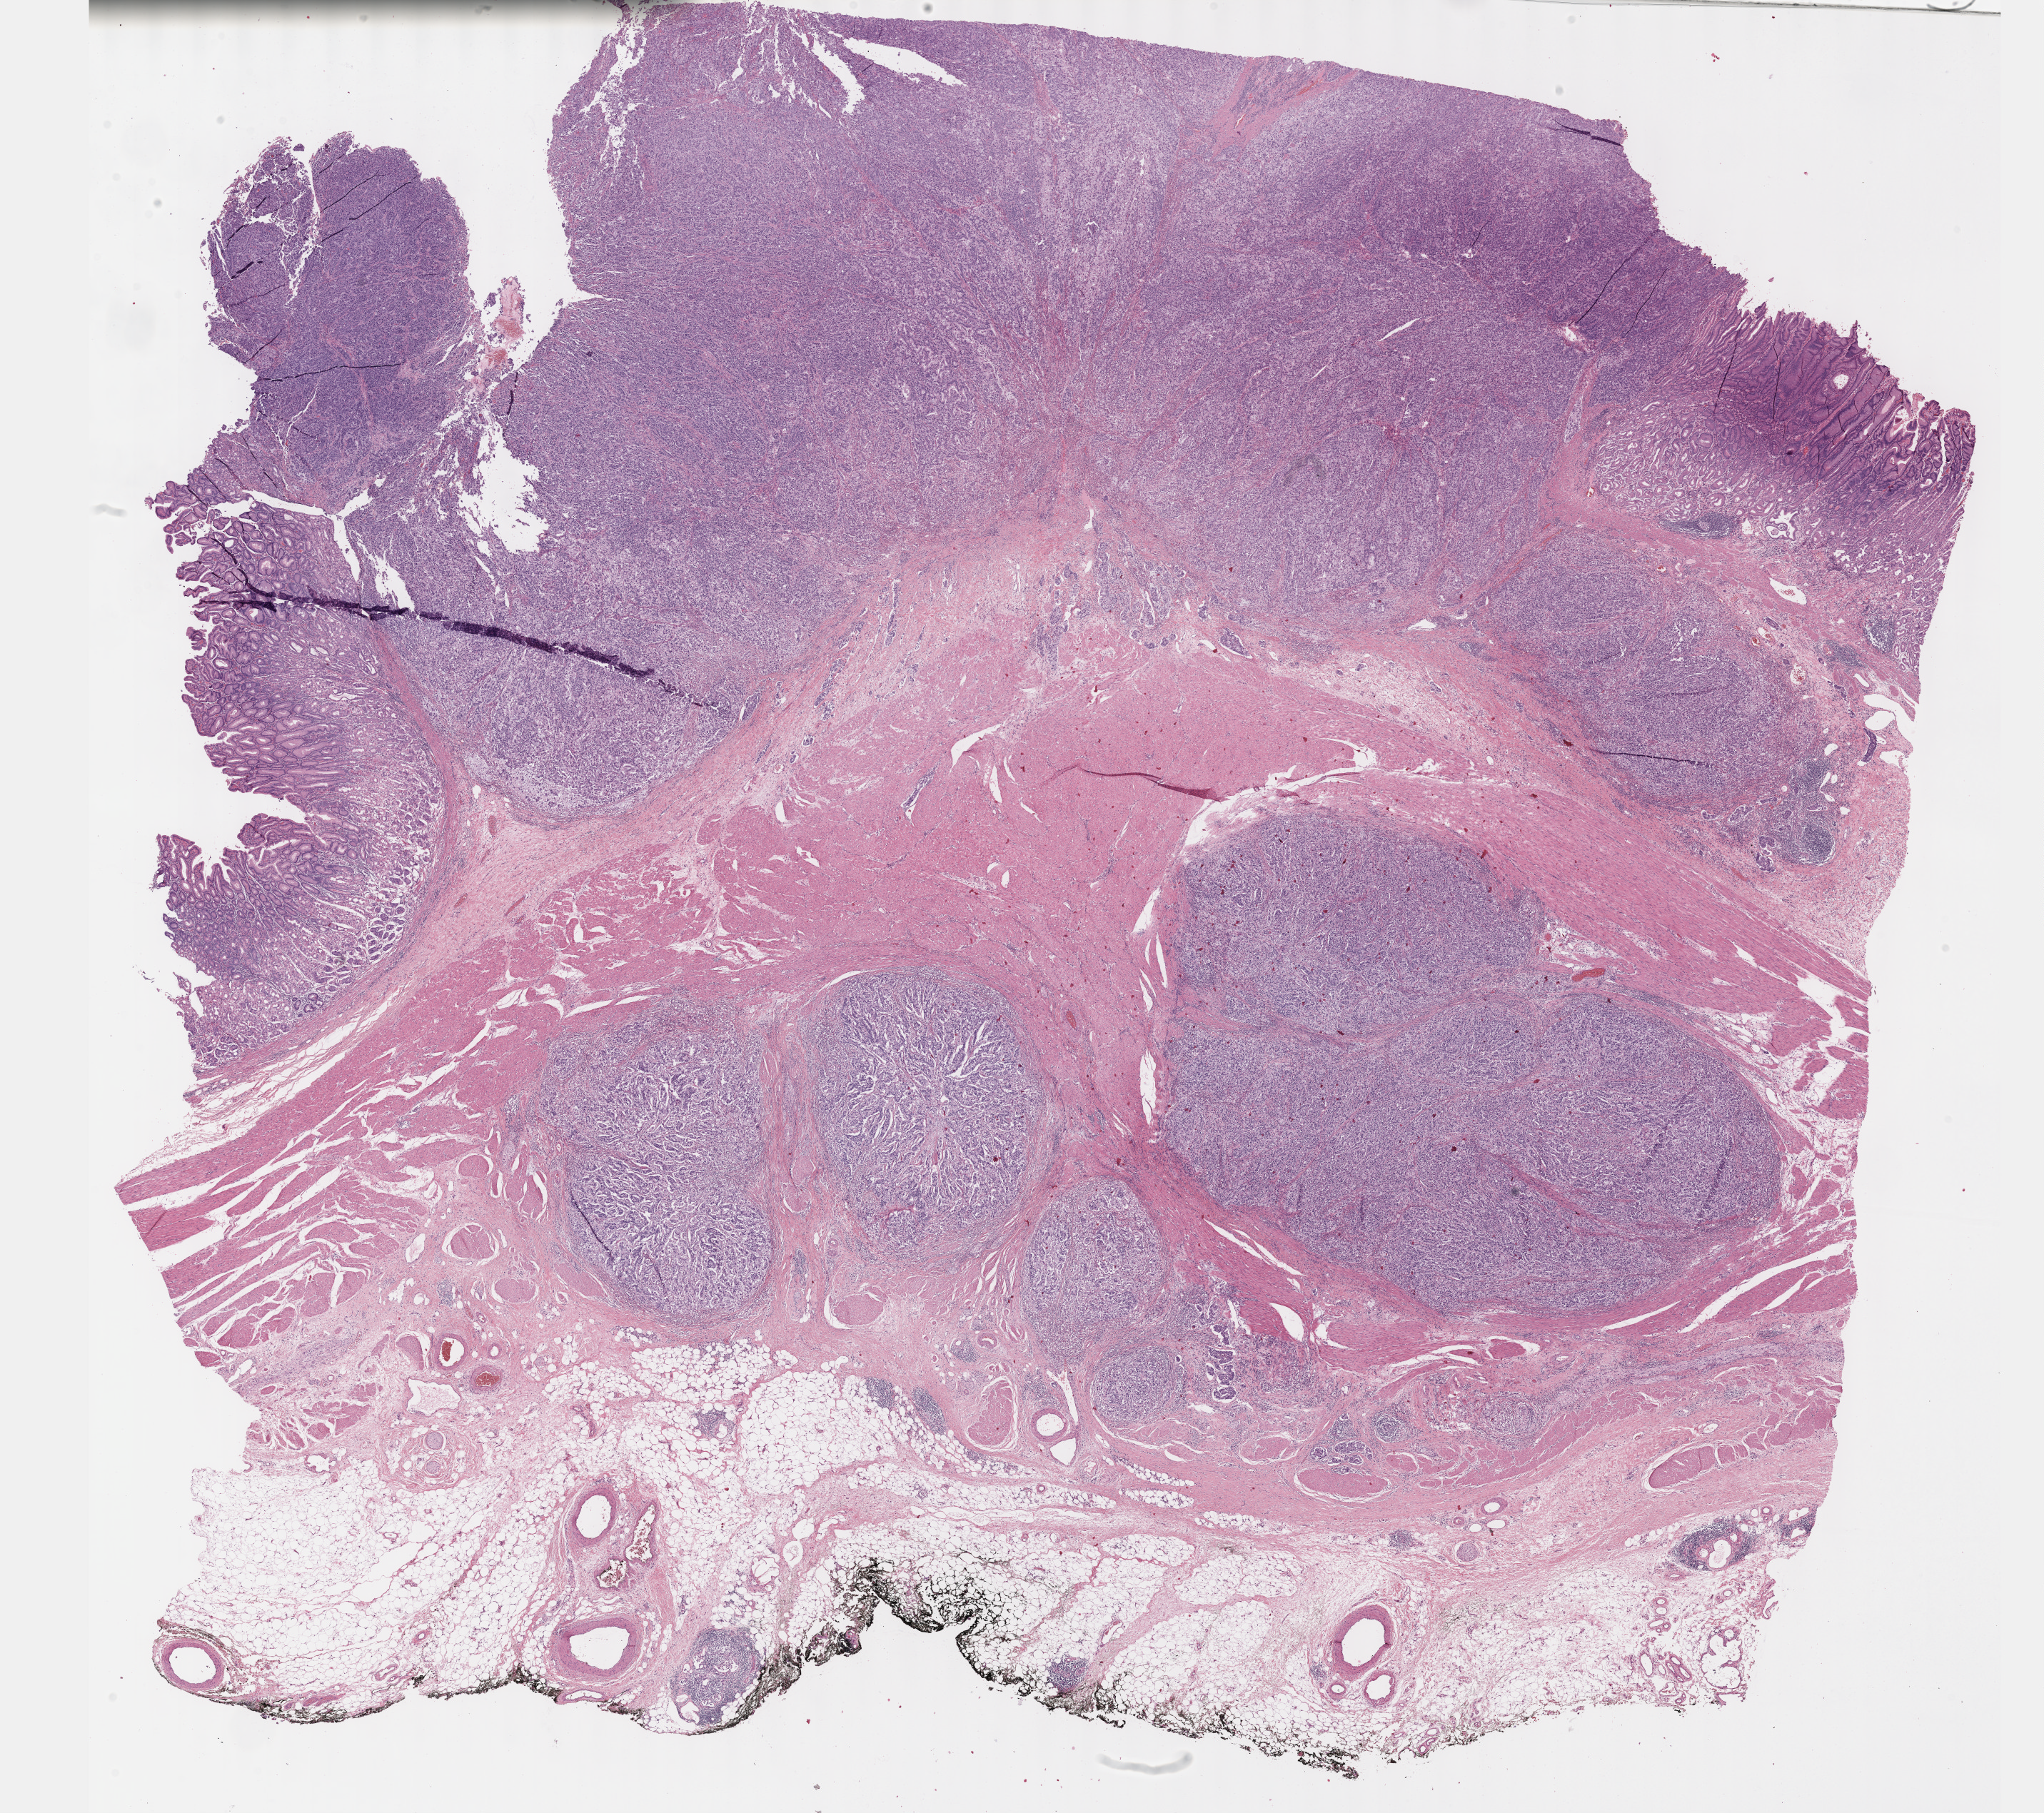
H&E-stained whole-slide image, whole scanned area (about 23.1 x 20.5 mm) shown as a low-resolution overview; formalin-fixed paraffin-embedded (FFPE) diagnostic section; stomach, primary tumour sample. Patient: male, age at initial diagnosis 73 years. Histologic grade: G3 (poorly differentiated).
AJCC pathologic stage: IIIB (6th edition). Pathologic diagnosis: Carcinoma, diffuse type (cardia, NOS).